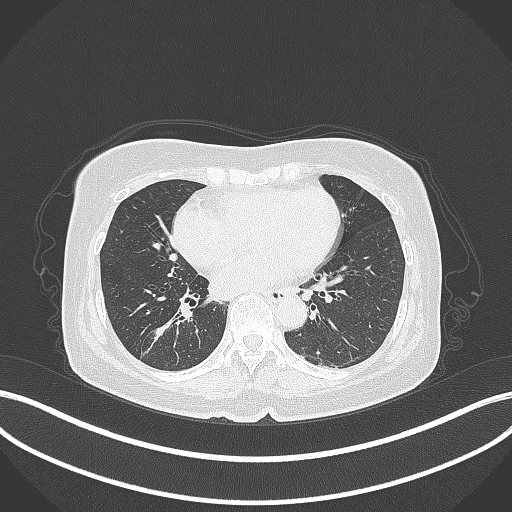
Chest CT, one axial slice; slice 168 of 429 in the series (ordered by position); reconstruction kernel B70f; 120 kVp; lung window (W 1500 / L -600 HU); 1 mm slice thickness; 512 × 512 image matrix, field of view 400 × 400 mm. Patient: female, 67 years. From the clinical record (not read from this slice): clinical TNM (as recorded): T1c N1 M0.
Outlined on this slice (rectangle marked by the reading radiologist):
- lung tumour (recorded histology: adenocarcinoma): box from (x=142, y=304) to (x=201, y=358) px